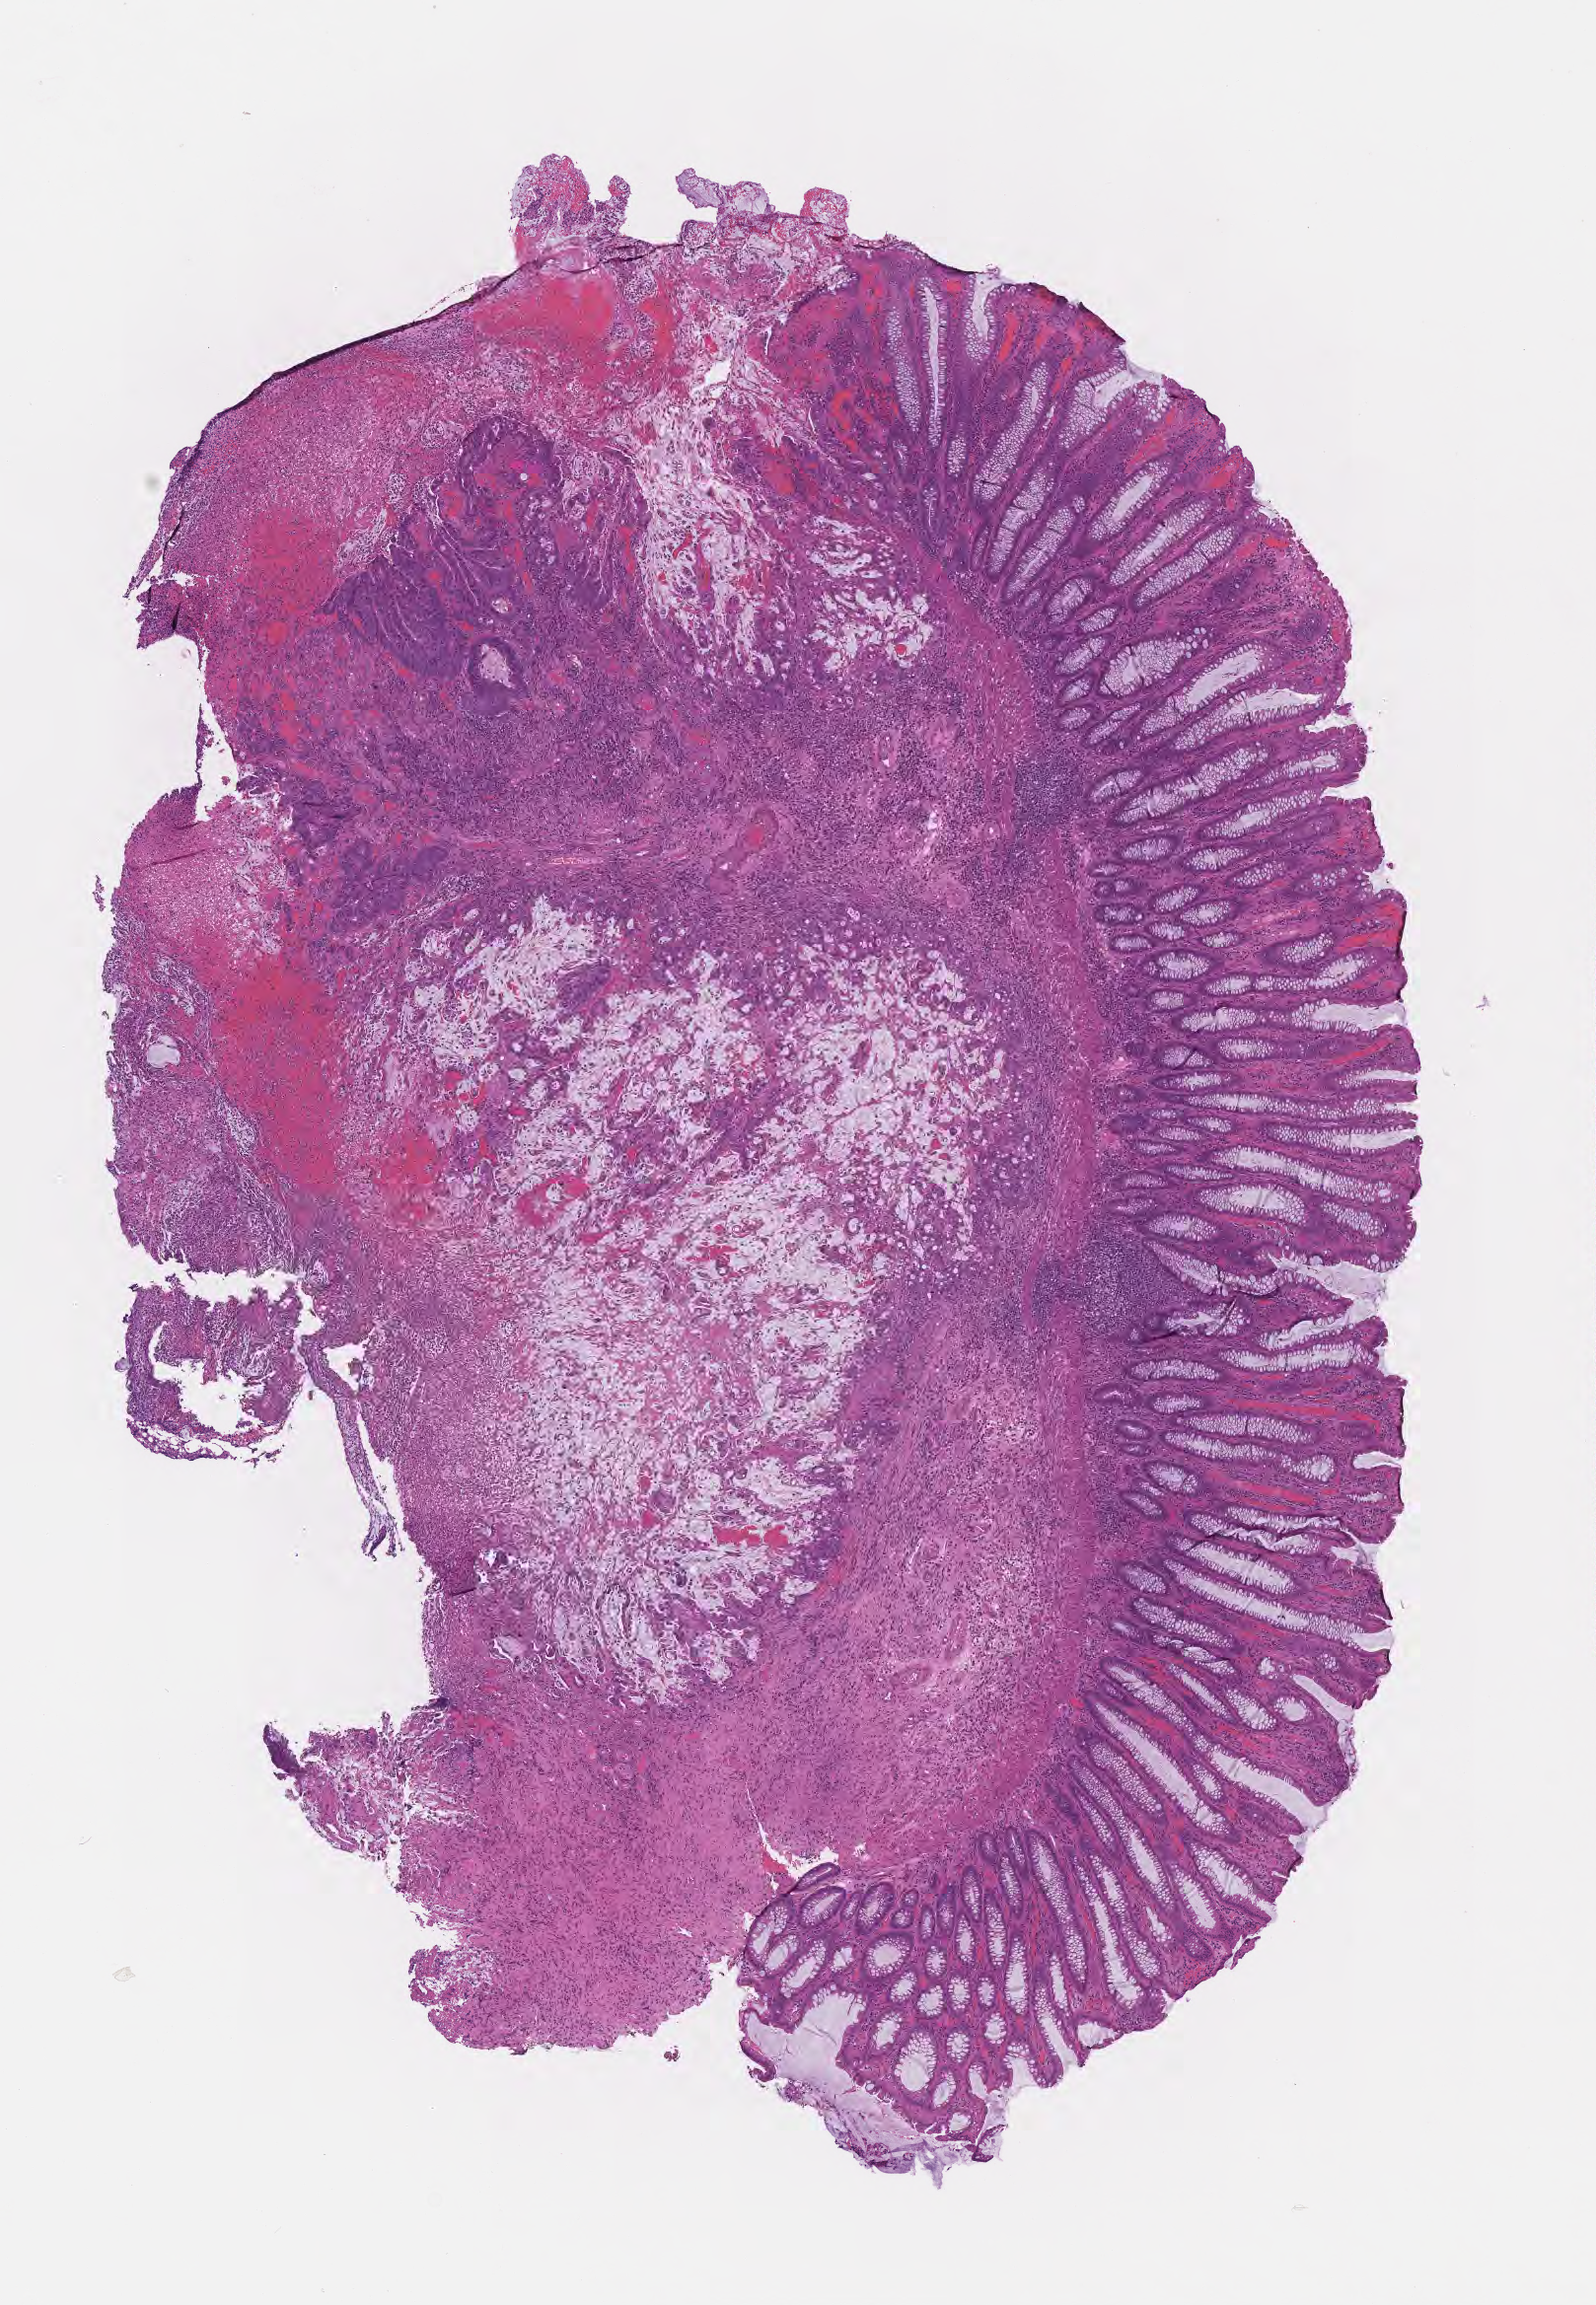
Whole-slide image, hematoxylin and eosin (H&E) stain — whole scanned area (about 6.5 x 9.4 mm) shown as a low-resolution overview, formalin-fixed paraffin-embedded section, specimen: primary tumor, site: sigmoid colon. Patient: male, age at initial diagnosis 55 years. Slide review estimates, as recorded: tumor cells 70%, tumor nuclei 70%, stromal cells 23%, necrosis 0%, normal cells 7%. Infiltration values recorded for this section: lymphocyte infiltration 8%, monocyte infiltration 1%, neutrophil infiltration 7%.
Diagnosis: Mucinous adenocarcinoma. AJCC pathologic stage: Stage IIIC. Section: bottom of the tissue portion.